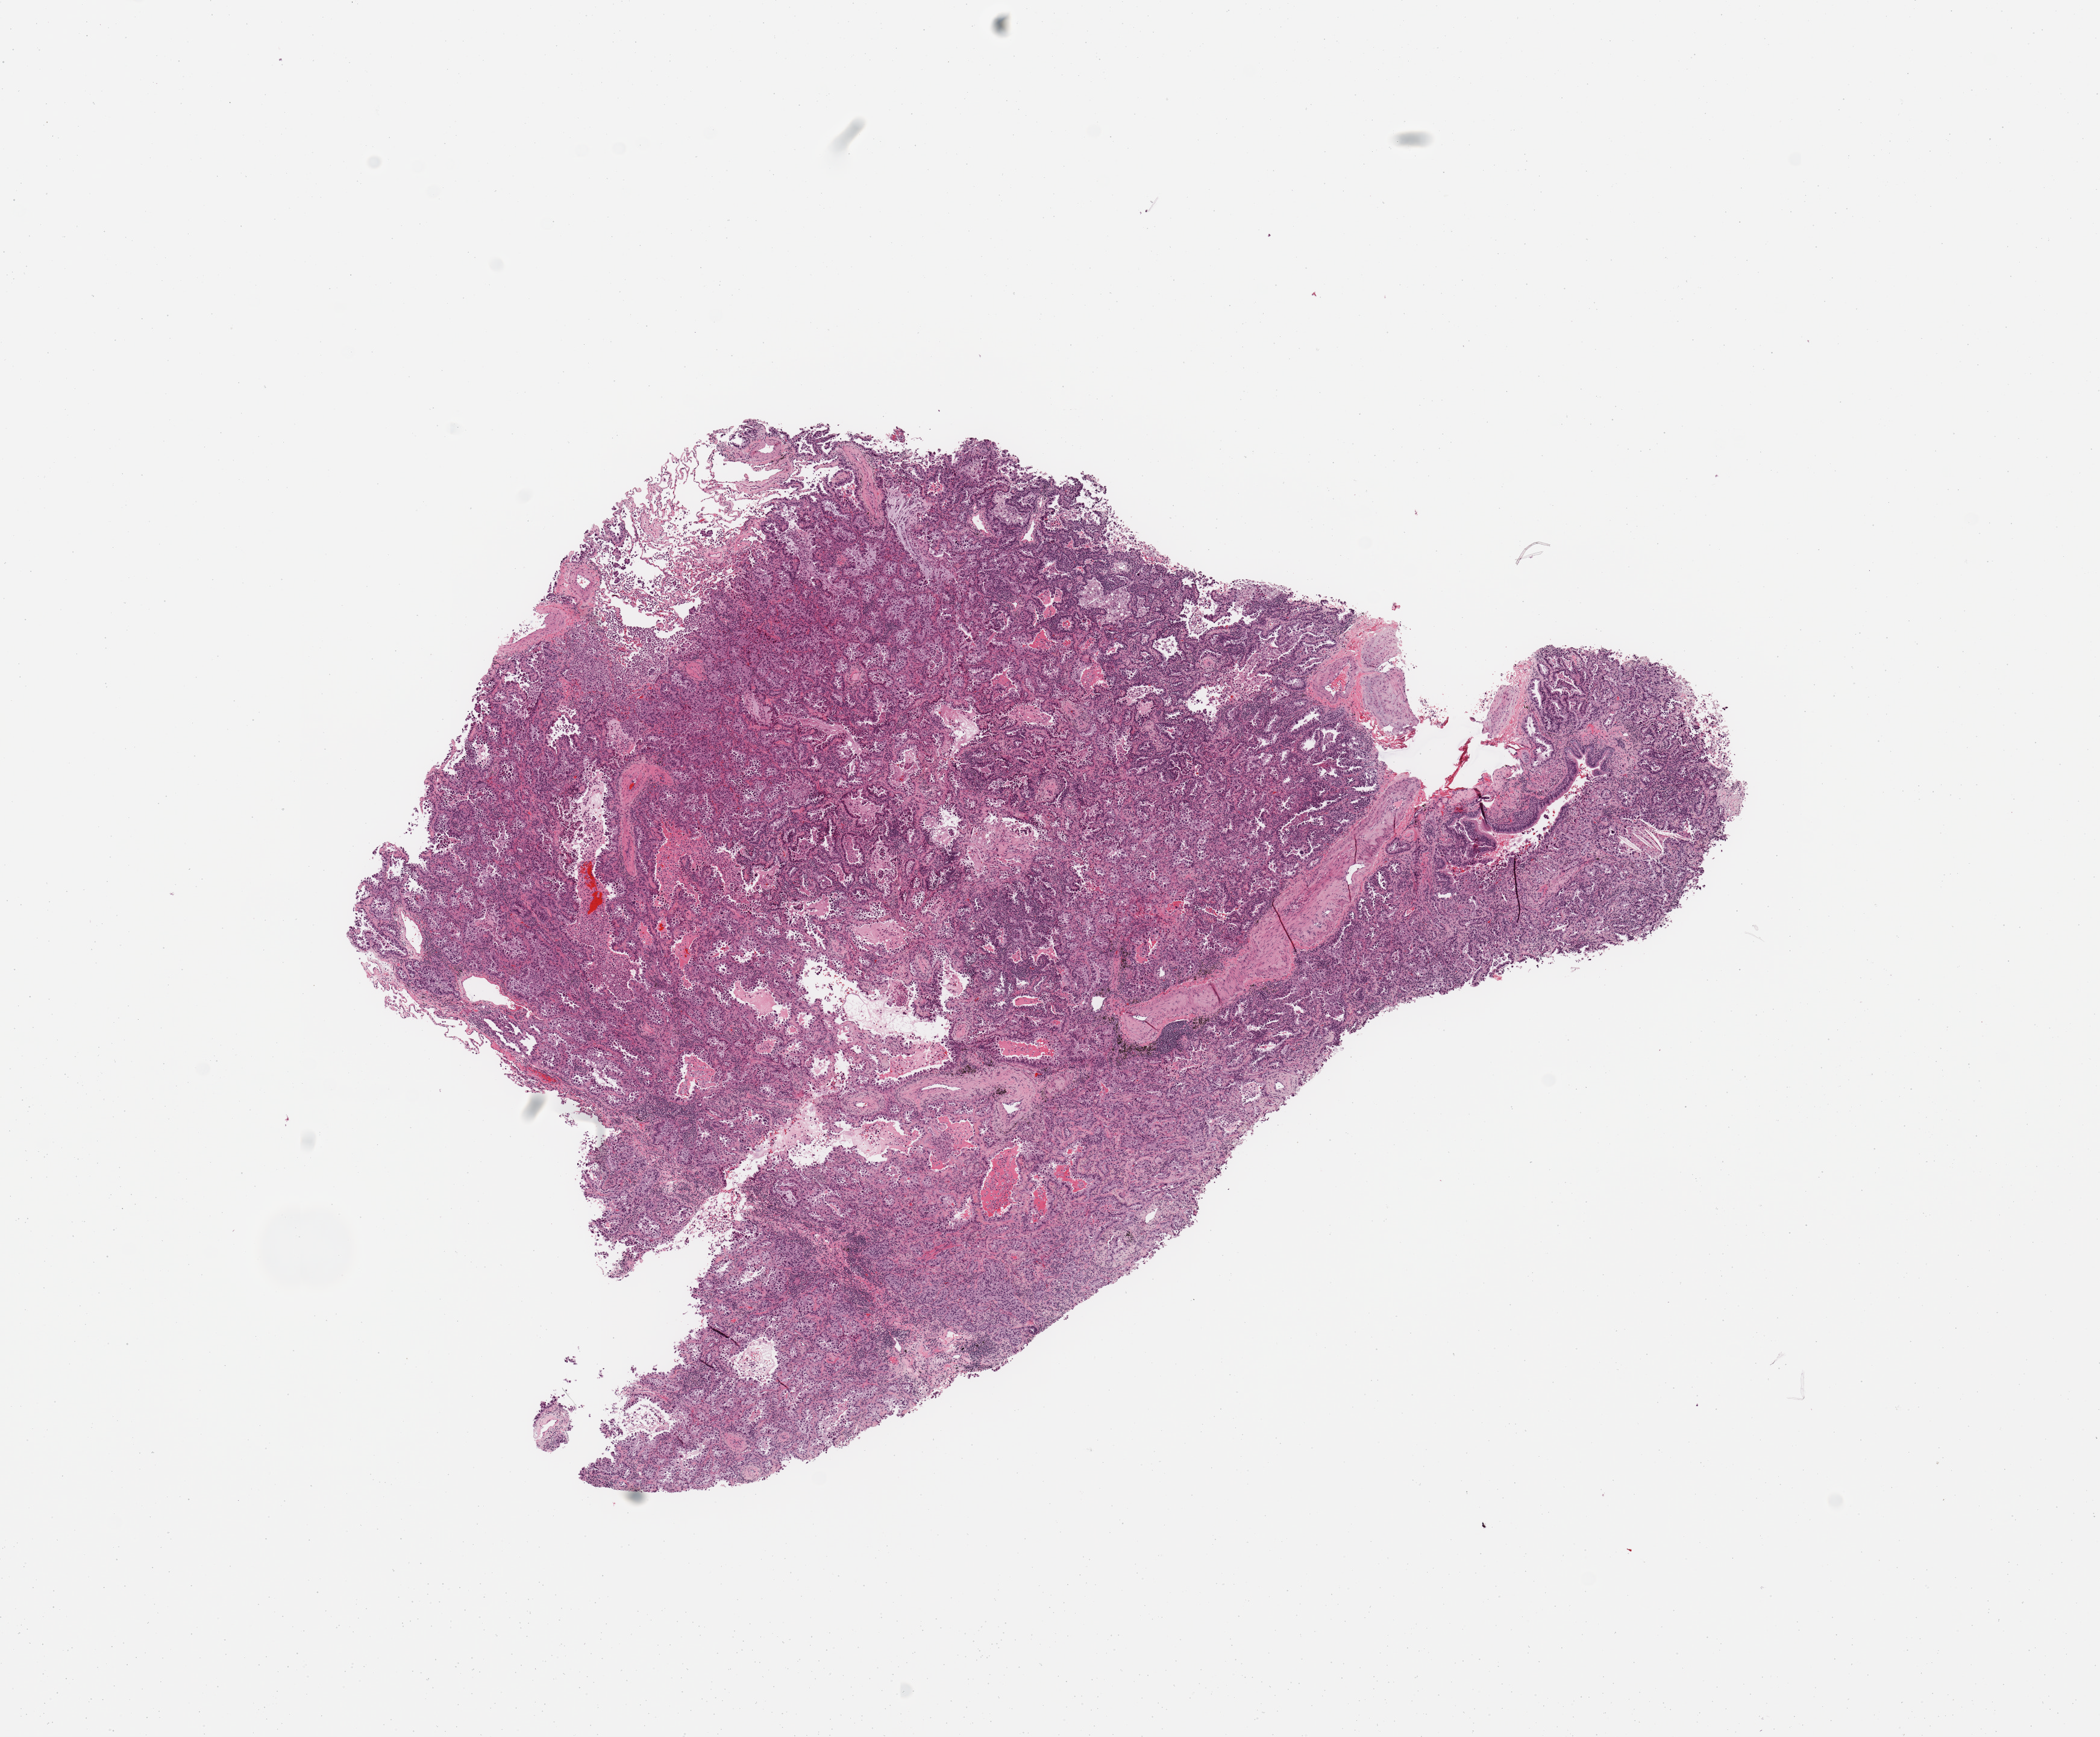
H&E whole-slide image, whole scanned area (about 13.8 x 11.4 mm, from a 20x scan) shown as a low-resolution overview, tumour tissue sample, sampled site: lung. Male, 77 y/o. Histologic grade: G2 (moderately differentiated). Composition of this section per pathologist review: tumour nuclei 80%, necrosis 5%.
AJCC pathologic stage: IIIA. Histologic diagnosis: Adenocarcinoma, NOS. Primary tumour site (as recorded): right lower lobe.